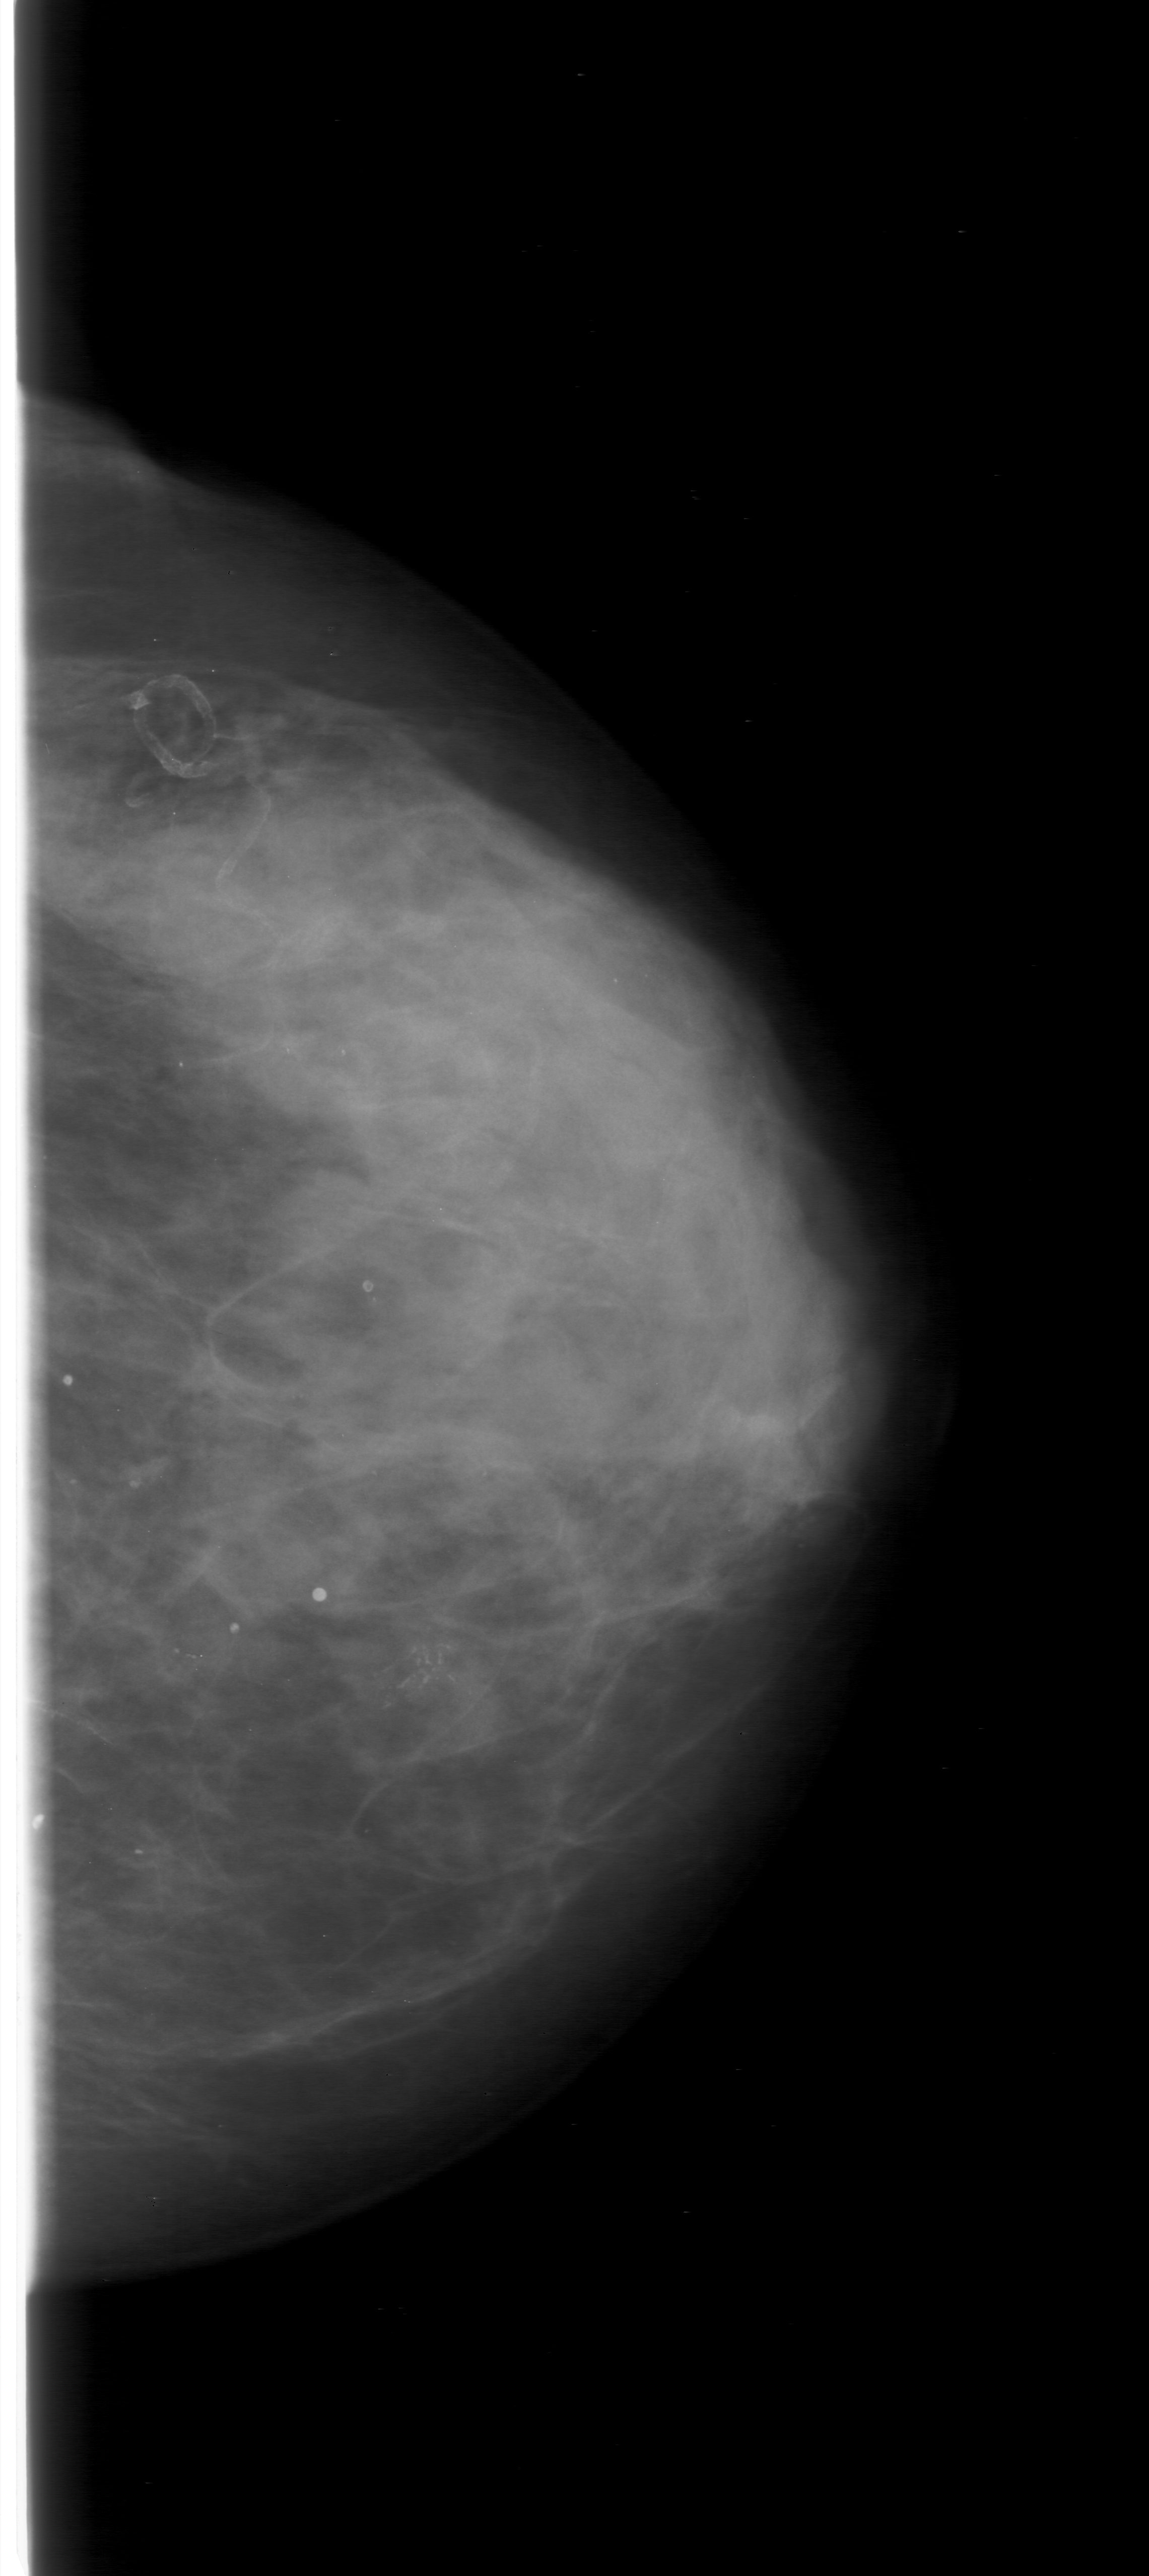
Mammogram (digitized film); left breast; craniocaudal (CC) view; BI-RADS breast density category 3 (scale 1–4); 1149 × 2576 image matrix.
Marked abnormalities (boxes around the expert regions of interest):
- calcifications, morphology fine linear branching, distribution clustered; BI-RADS assessment category 5; pathology (as recorded): malignant: bounding box (x1, y1, x2, y2) in pixels: (281, 1524, 635, 1844)